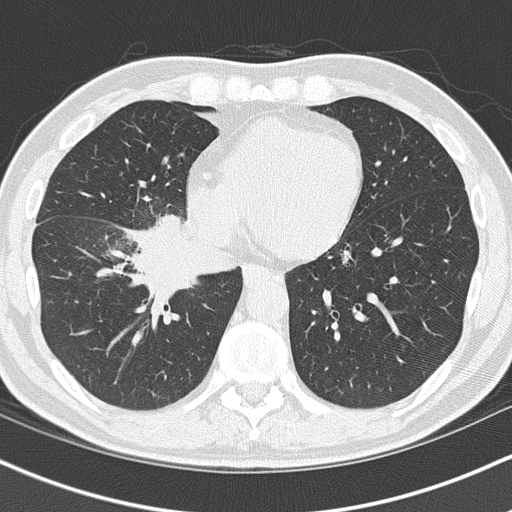
Low-dose screening chest CT, one axial slice. Position 46 of 151 along the scan axis. Lung window (W 1500 / L -600 HU). 2 mm slice thickness. 512 × 512 image matrix.
Annotated regions visible in this slice (outlined manually by an expert reader):
- lesion 1 (tumor, hilum of right lung): bounding box [x1, y1, x2, y2] px = [129, 216, 198, 298]